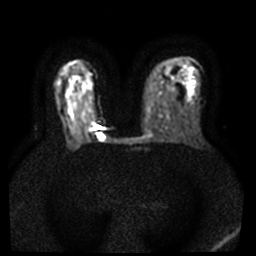
Breast MRI, one axial slice. Slice 23 of 40 in the series (ordered by position). Diffusion-weighted series; image 2 of 4 stored at this slice position (different b-values; order by instance number). 3 T. 5 mm slice thickness. 256 × 256 image matrix. Female patient.
Annotated regions visible in this slice (outlined manually by an expert reader):
- tumour on diffusion-weighted imaging: box from (x=97, y=134) to (x=104, y=141) px